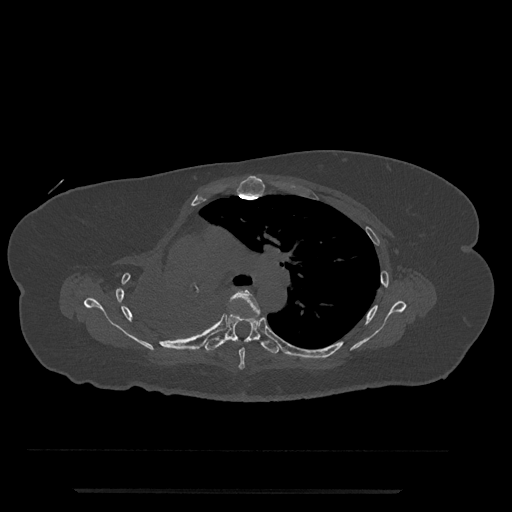
CT including the spine, one axial slice; slice 515 of 797 in the series (ordered by position); bone window (W 1800 / L 400 HU); 0.5 mm slice thickness; 512 × 512 image matrix, field of view 440 × 440 mm. Patient: female, 51 years. Case-level facts recorded for this patient, not image findings: primary cancer: neuro; vertebrae with lytic lesions (as recorded): T8.
Outlined on this slice (semi-automatic segmentation, software-assisted and operator-edited):
- T5 vertebra: bounding box (x1, y1, x2, y2) in pixels: (229, 289, 264, 370)
- T6 vertebra: (205, 314, 280, 354)